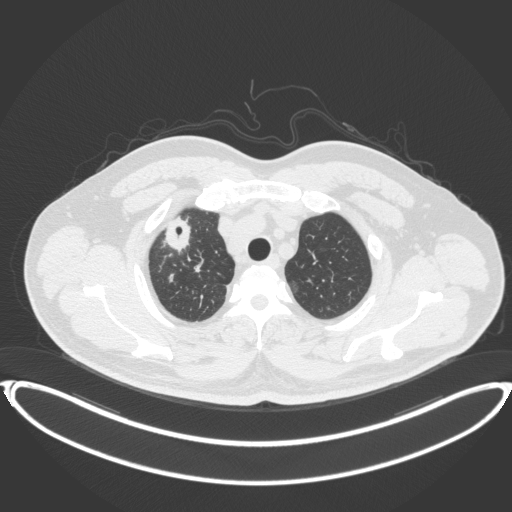
Chest CT, one axial slice; position 331 of 399 along the scan axis; lung window (W 1500 / L -600 HU); 512 × 512 image matrix, field of view 445 × 445 mm. Male patient, age 53 years. Case-level facts recorded for this patient, not image findings: clinical TNM (as recorded): T2a N0 M0.
Annotated regions visible in this slice (rectangle marked by the reading radiologist):
- lung tumour (recorded histology: adenocarcinoma): box from (x=165, y=210) to (x=196, y=256) px